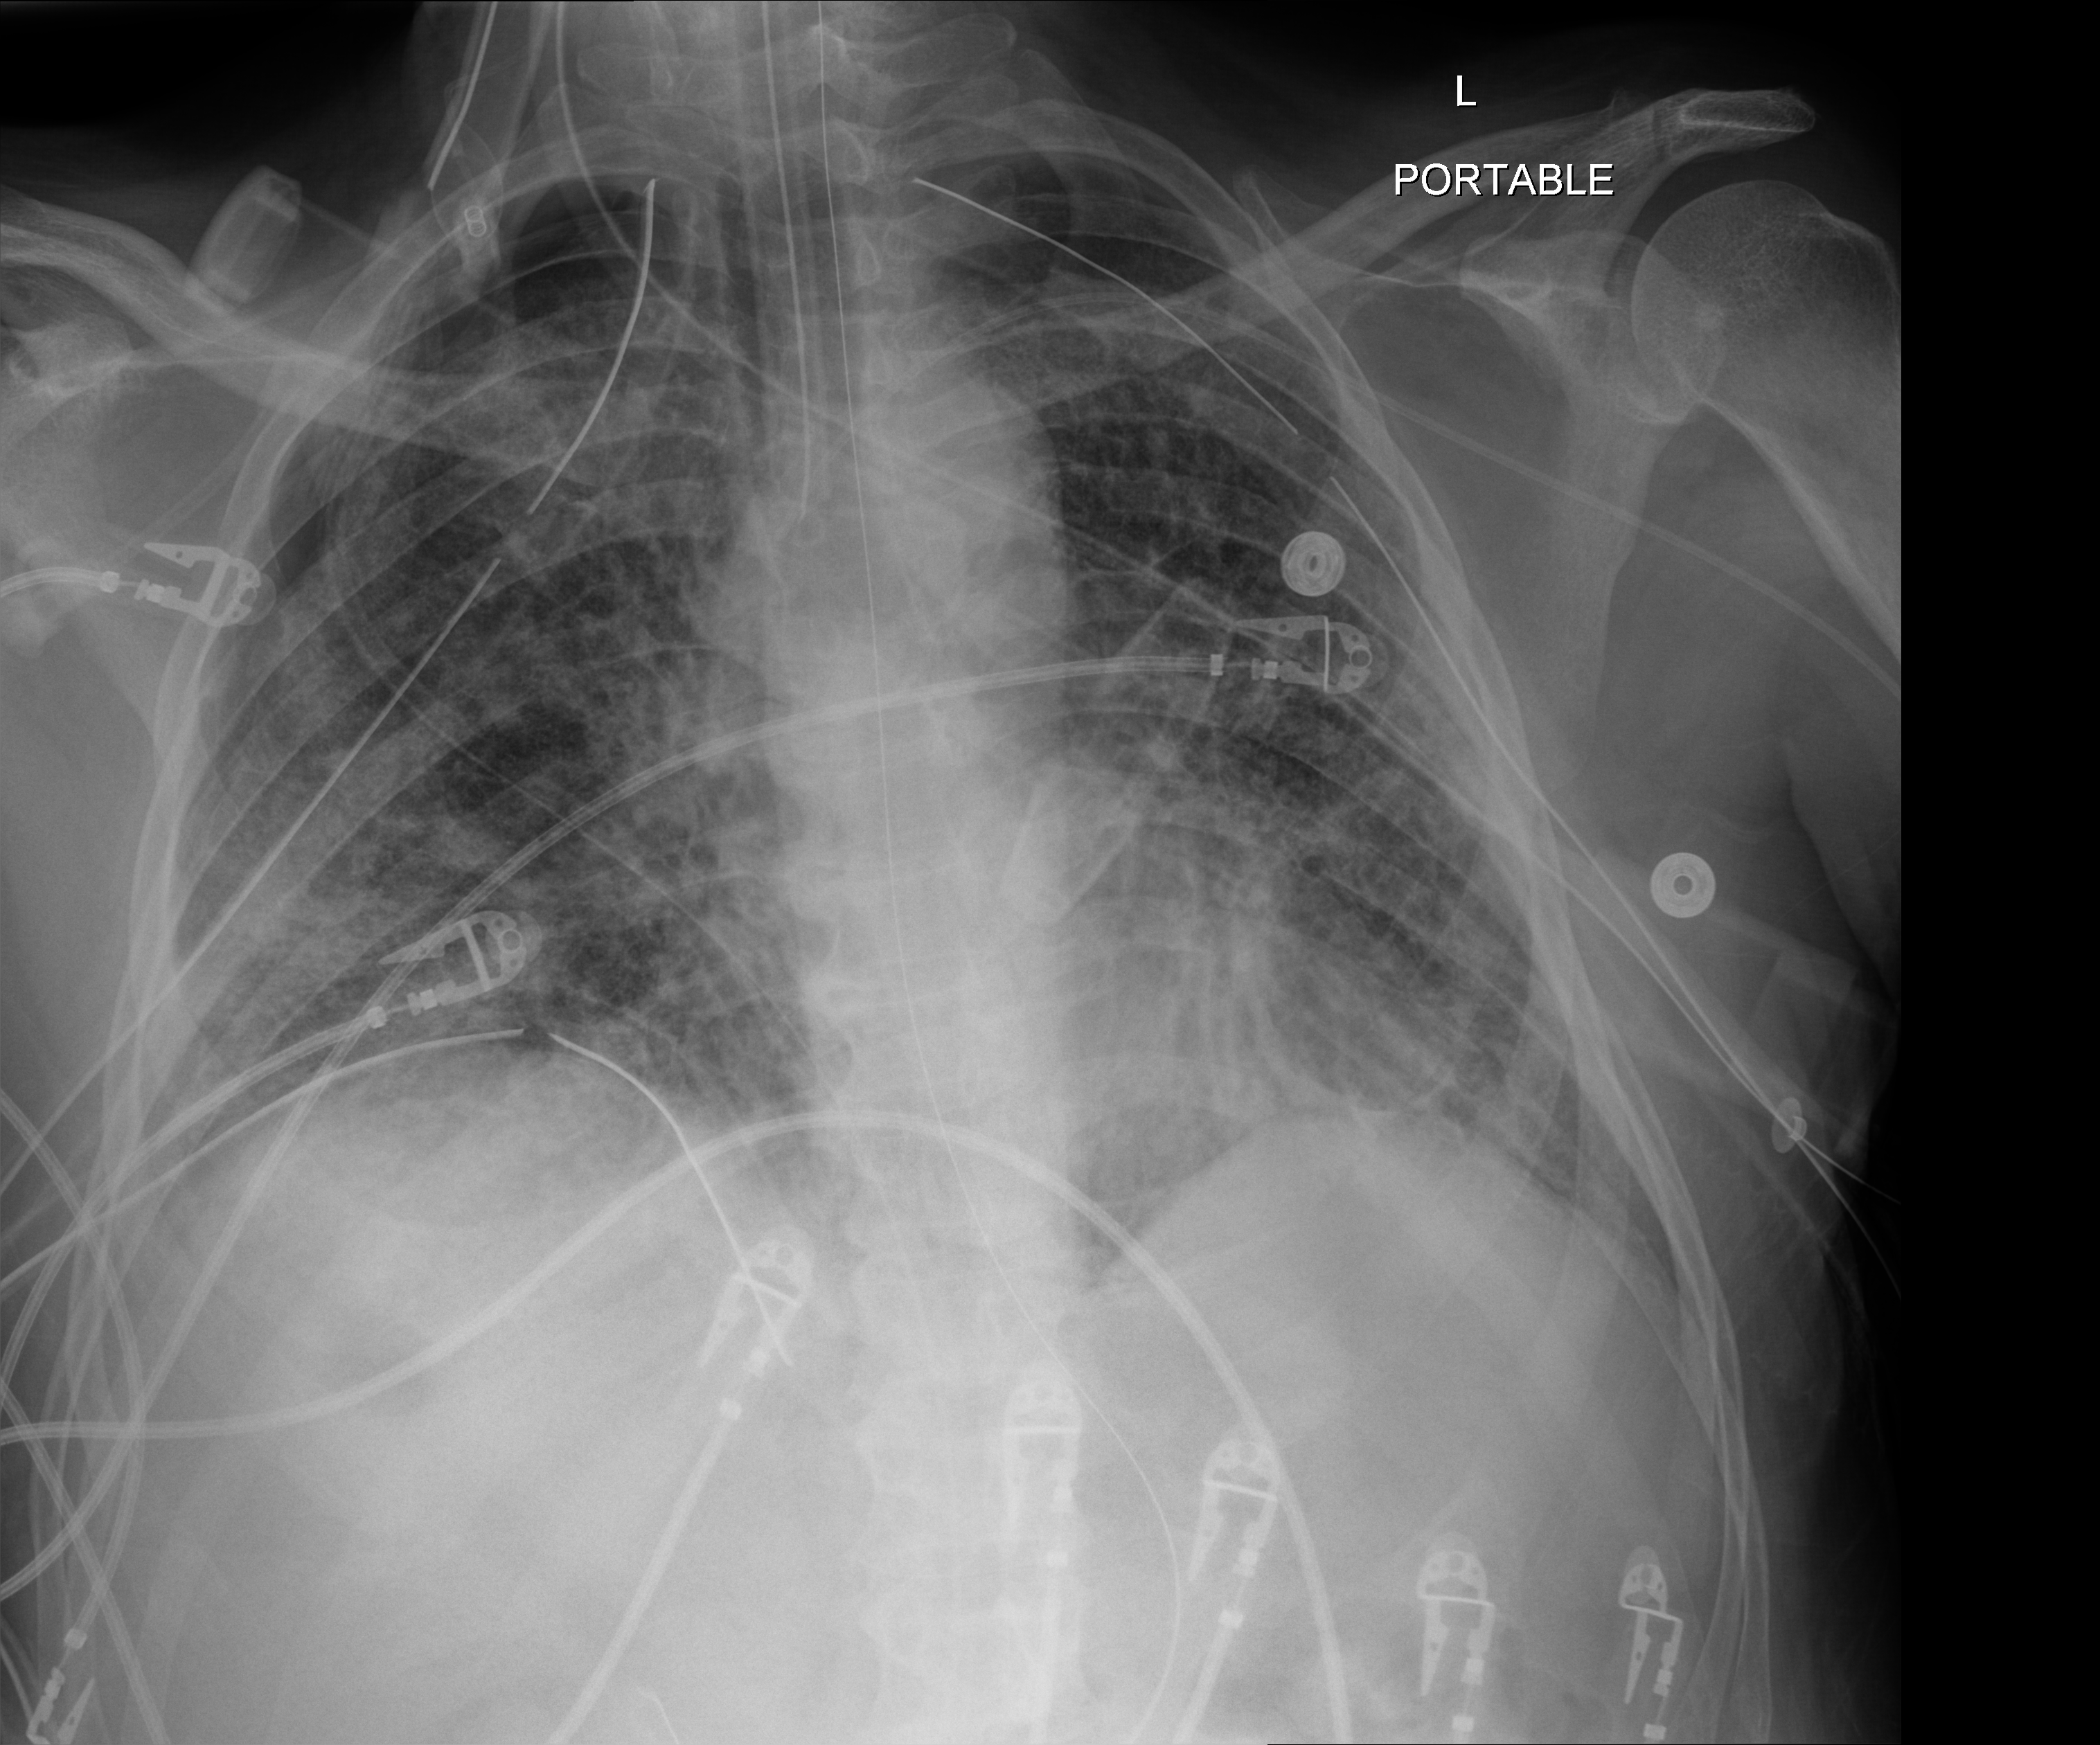
Portable chest radiograph; anteroposterior (AP) projection. Male patient hospitalised with COVID-19, age 18–59 years.
From the hospital-stay record, not from the radiograph (when in the stay this image was taken is not recorded): mechanically ventilated during this hospital stay: yes; admitted to intensive care during this hospital stay: yes.